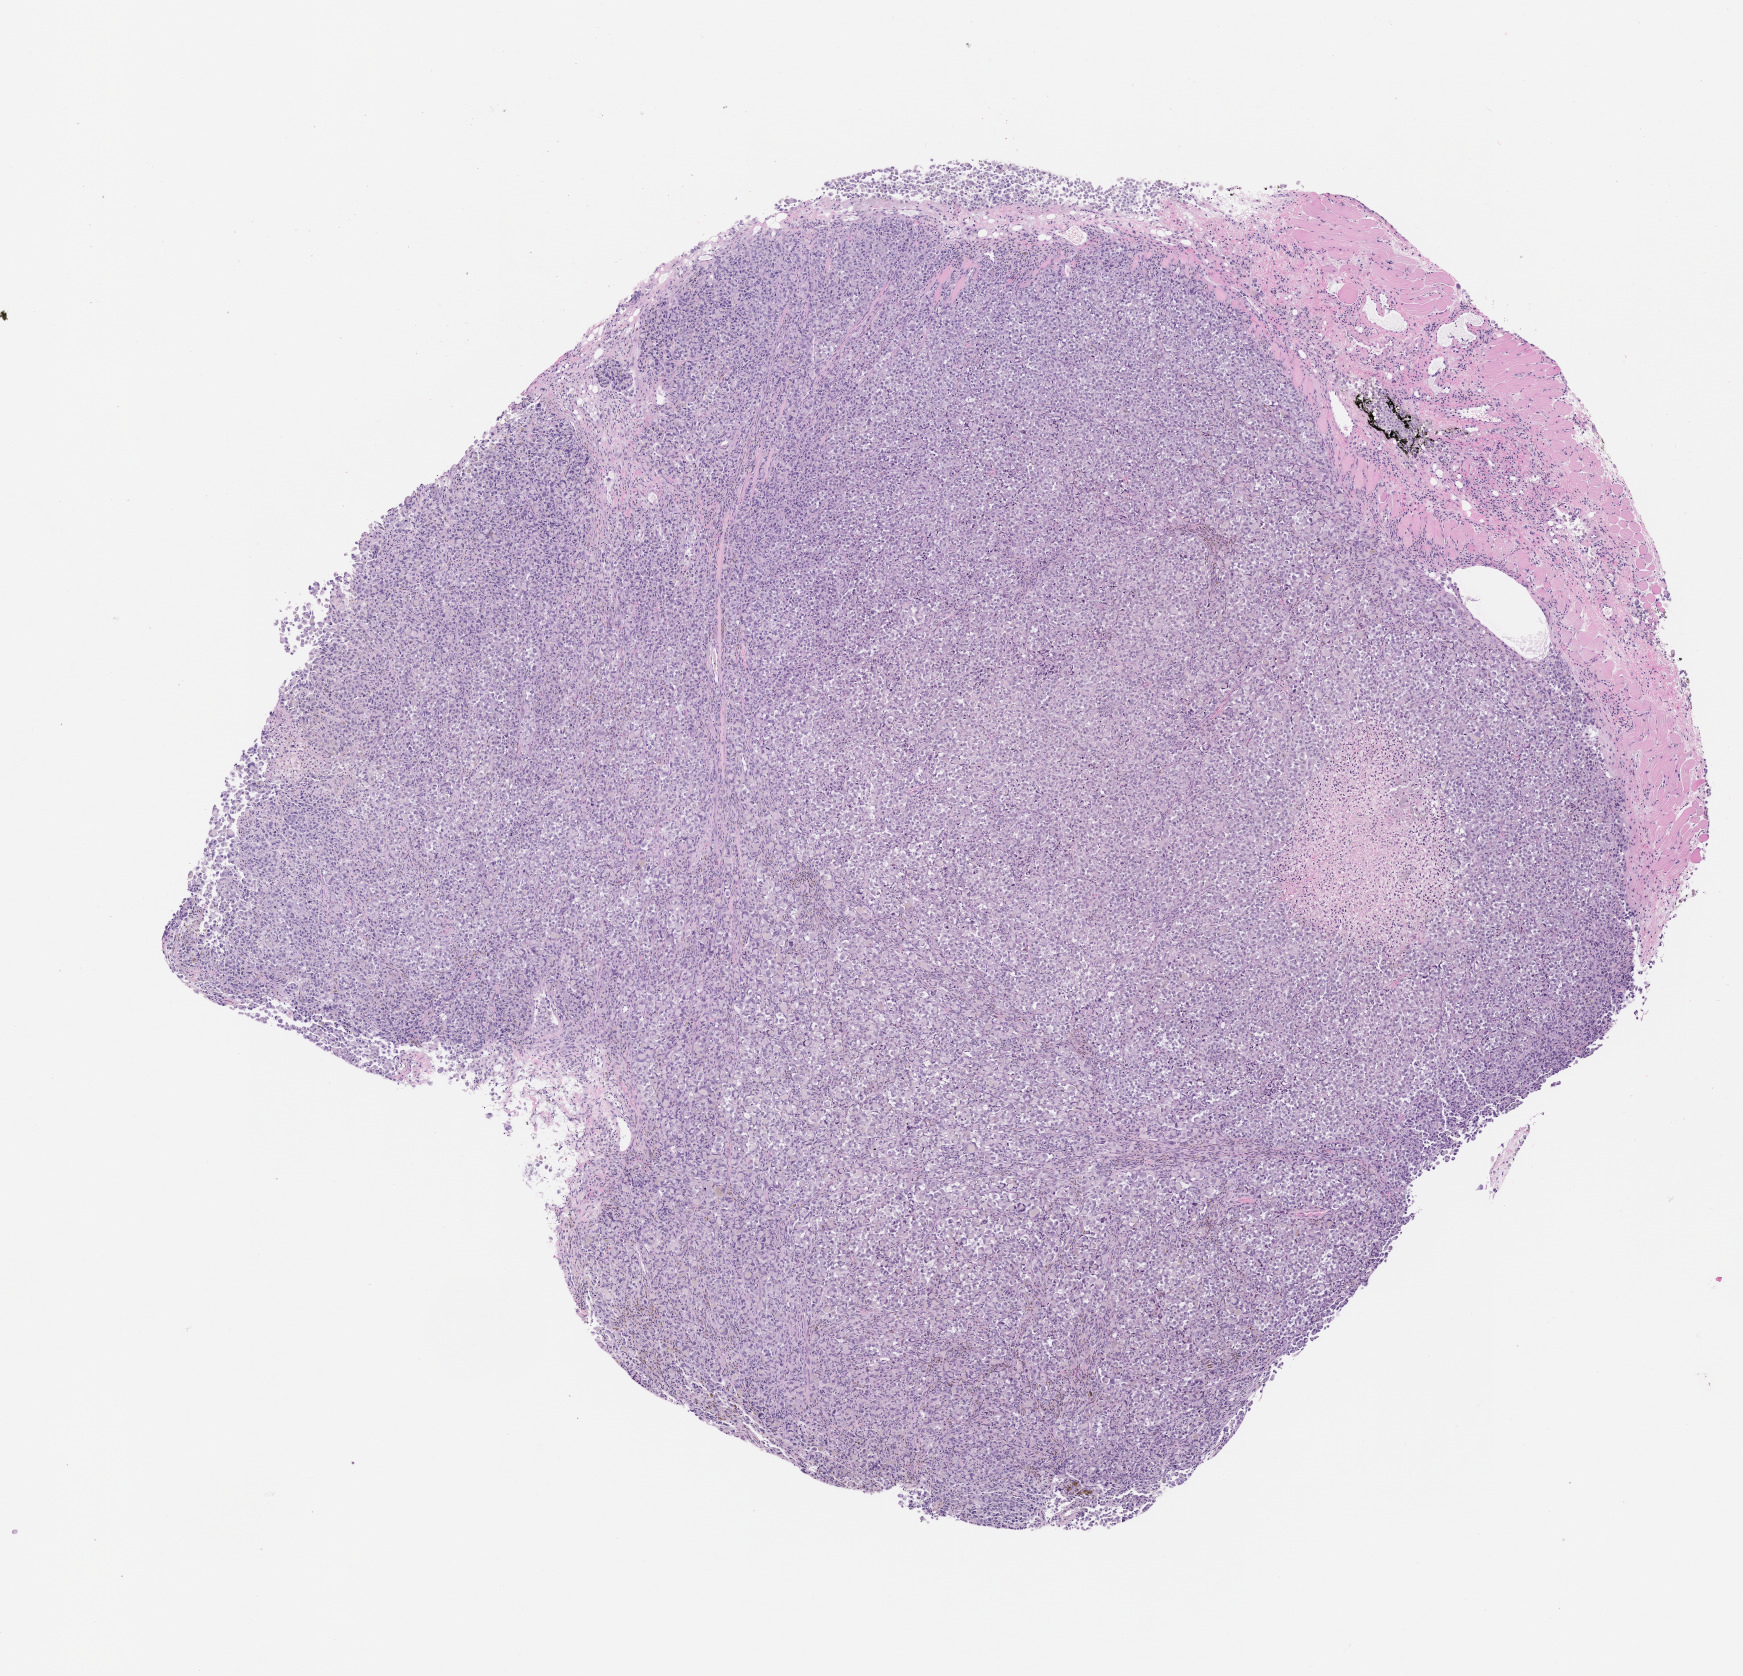
Whole-slide image, H&E: patient-derived xenograft (human tumor grown in a mouse), passage 2 — whole scanned area (about 7.0 x 6.7 mm) shown as a low-resolution overview; FFPE section; originating tumor site category: skin.
• originating patient diagnosis: Melanoma